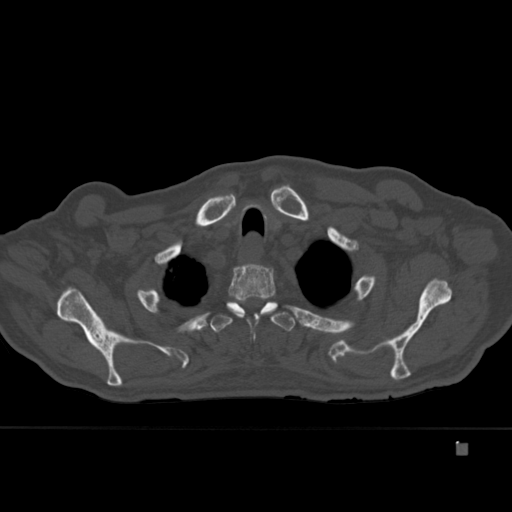
CT including the spine, one axial slice; bone window (W 1800 / L 400 HU); 1.5 mm slice thickness; 512 × 512 image matrix. Male patient, age 75 years. From the clinical record (not read from this slice): primary cancer: prostate.
Annotated regions visible in this slice (semi-automatic segmentation, software-assisted and operator-edited):
- T2 vertebra: bounding box [x1, y1, x2, y2] px = [227, 264, 278, 341]
- T3 vertebra: [210, 298, 296, 333]